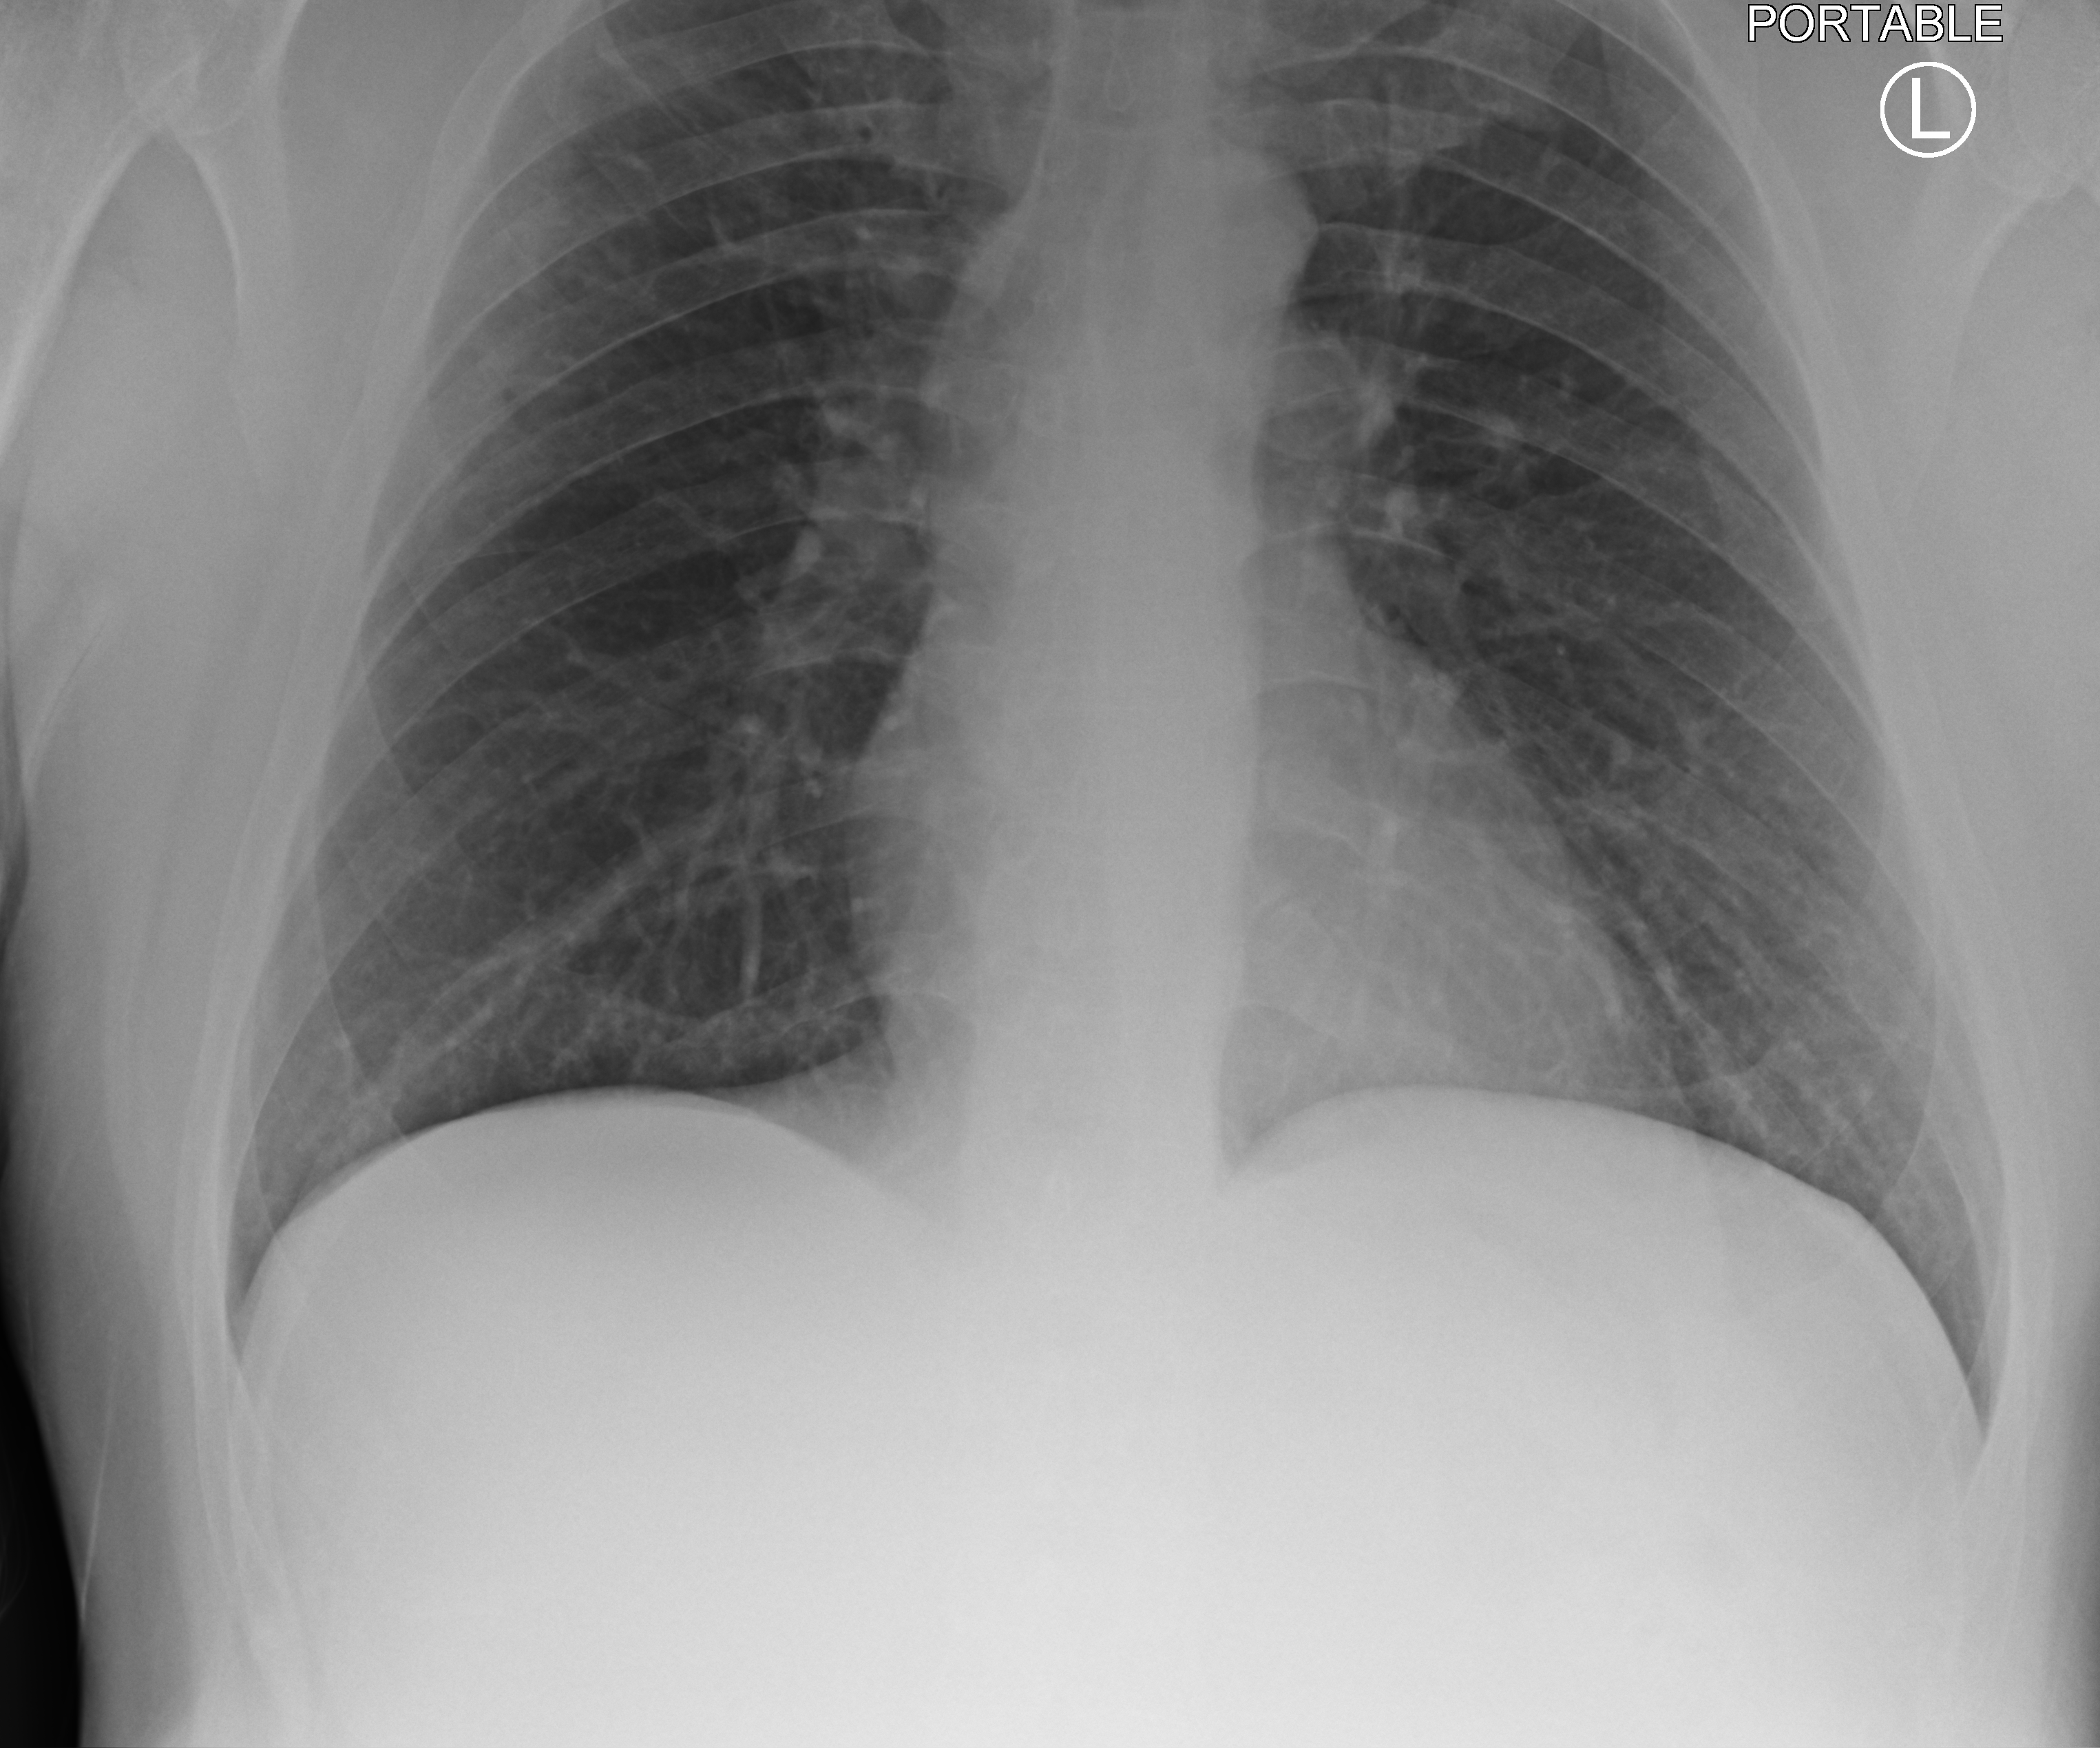
Chest X-ray (portable); anteroposterior (AP) projection. Patient hospitalised with COVID-19; male, aged 18–59 years.
Hospital-stay facts (about this admission, not read from this image; timing relative to this image not recorded): admitted to intensive care during this hospital stay: no; length of hospital stay: 1 day; mechanically ventilated during this hospital stay: no.